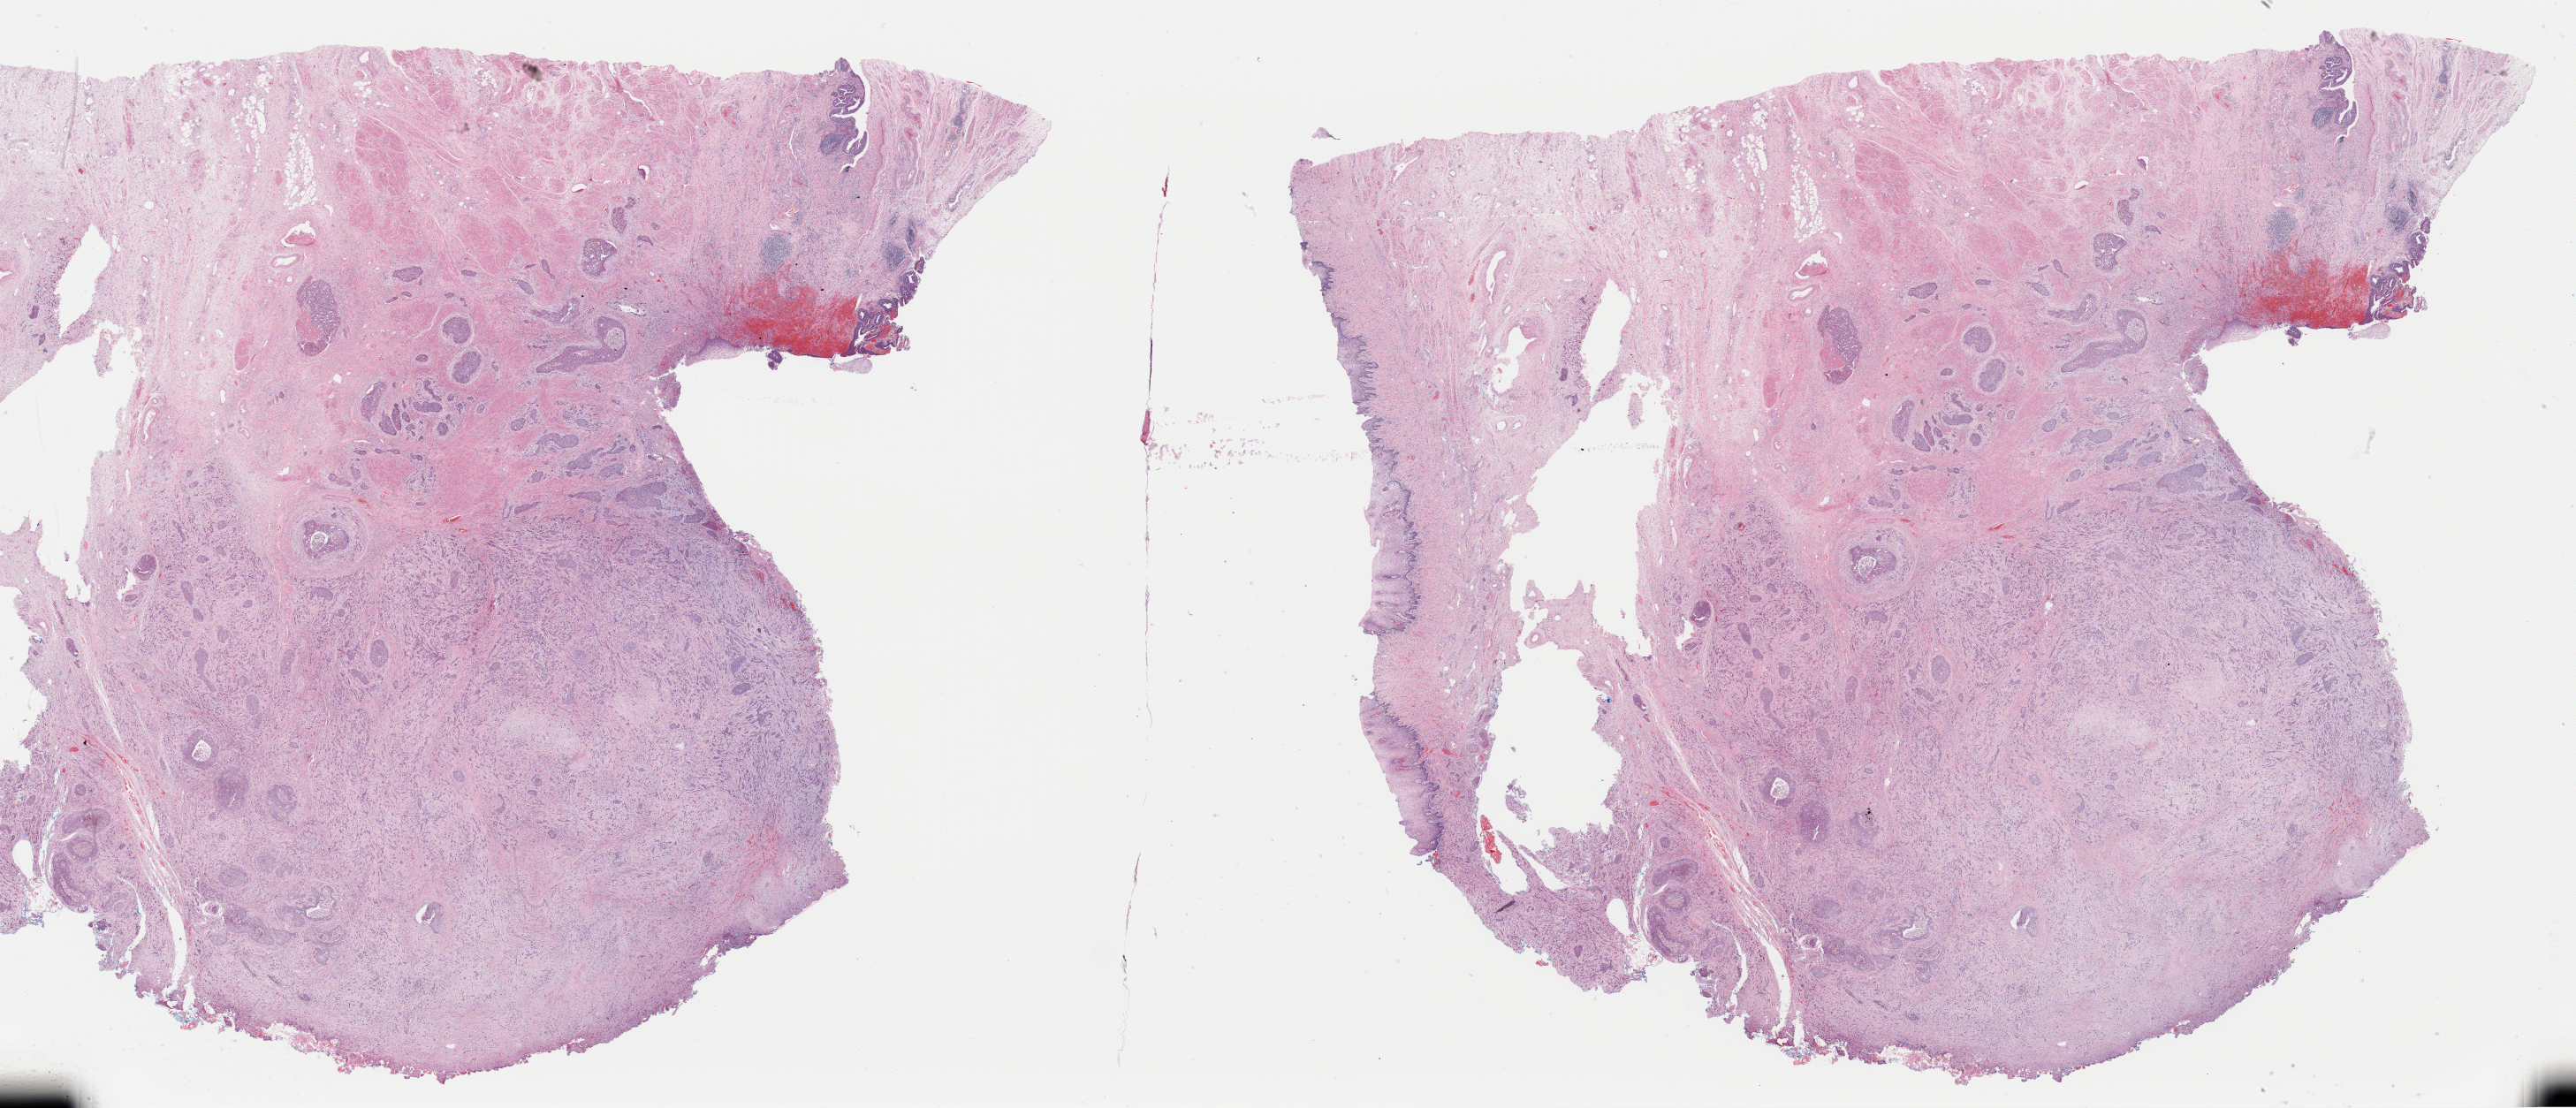
Whole-slide histology image, H&E — whole scanned area (about 46.1 x 19.8 mm) shown as a low-resolution overview, formalin-fixed paraffin-embedded (FFPE) diagnostic section, primary tumour sample from the bladder. Patient: female, age at initial diagnosis 80 years. Histologic grade: high grade.
AJCC pathologic stage: III (7th edition). Diagnosis: Transitional cell carcinoma (bladder neck).